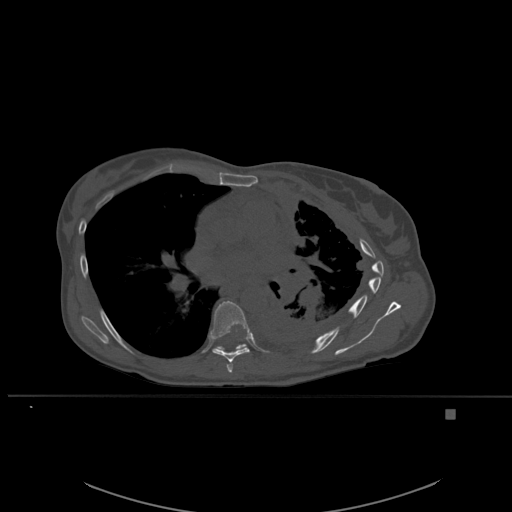
CT including the spine, one axial slice. Position 364 of 537 along the scan axis. Bone window (W 1800 / L 400 HU). 512 × 512 image matrix, field of view 440 × 440 mm. Female patient, age 45 years. Case-level facts recorded for this patient, not image findings: primary cancer: lung.
Structures marked on this image (semi-automatically segmented with operator editing):
- T6 vertebra: bounding box (x1, y1, x2, y2) in pixels: (226, 361, 233, 373)
- T7 vertebra: (211, 299, 250, 362)
- T8 vertebra: (215, 344, 248, 352)